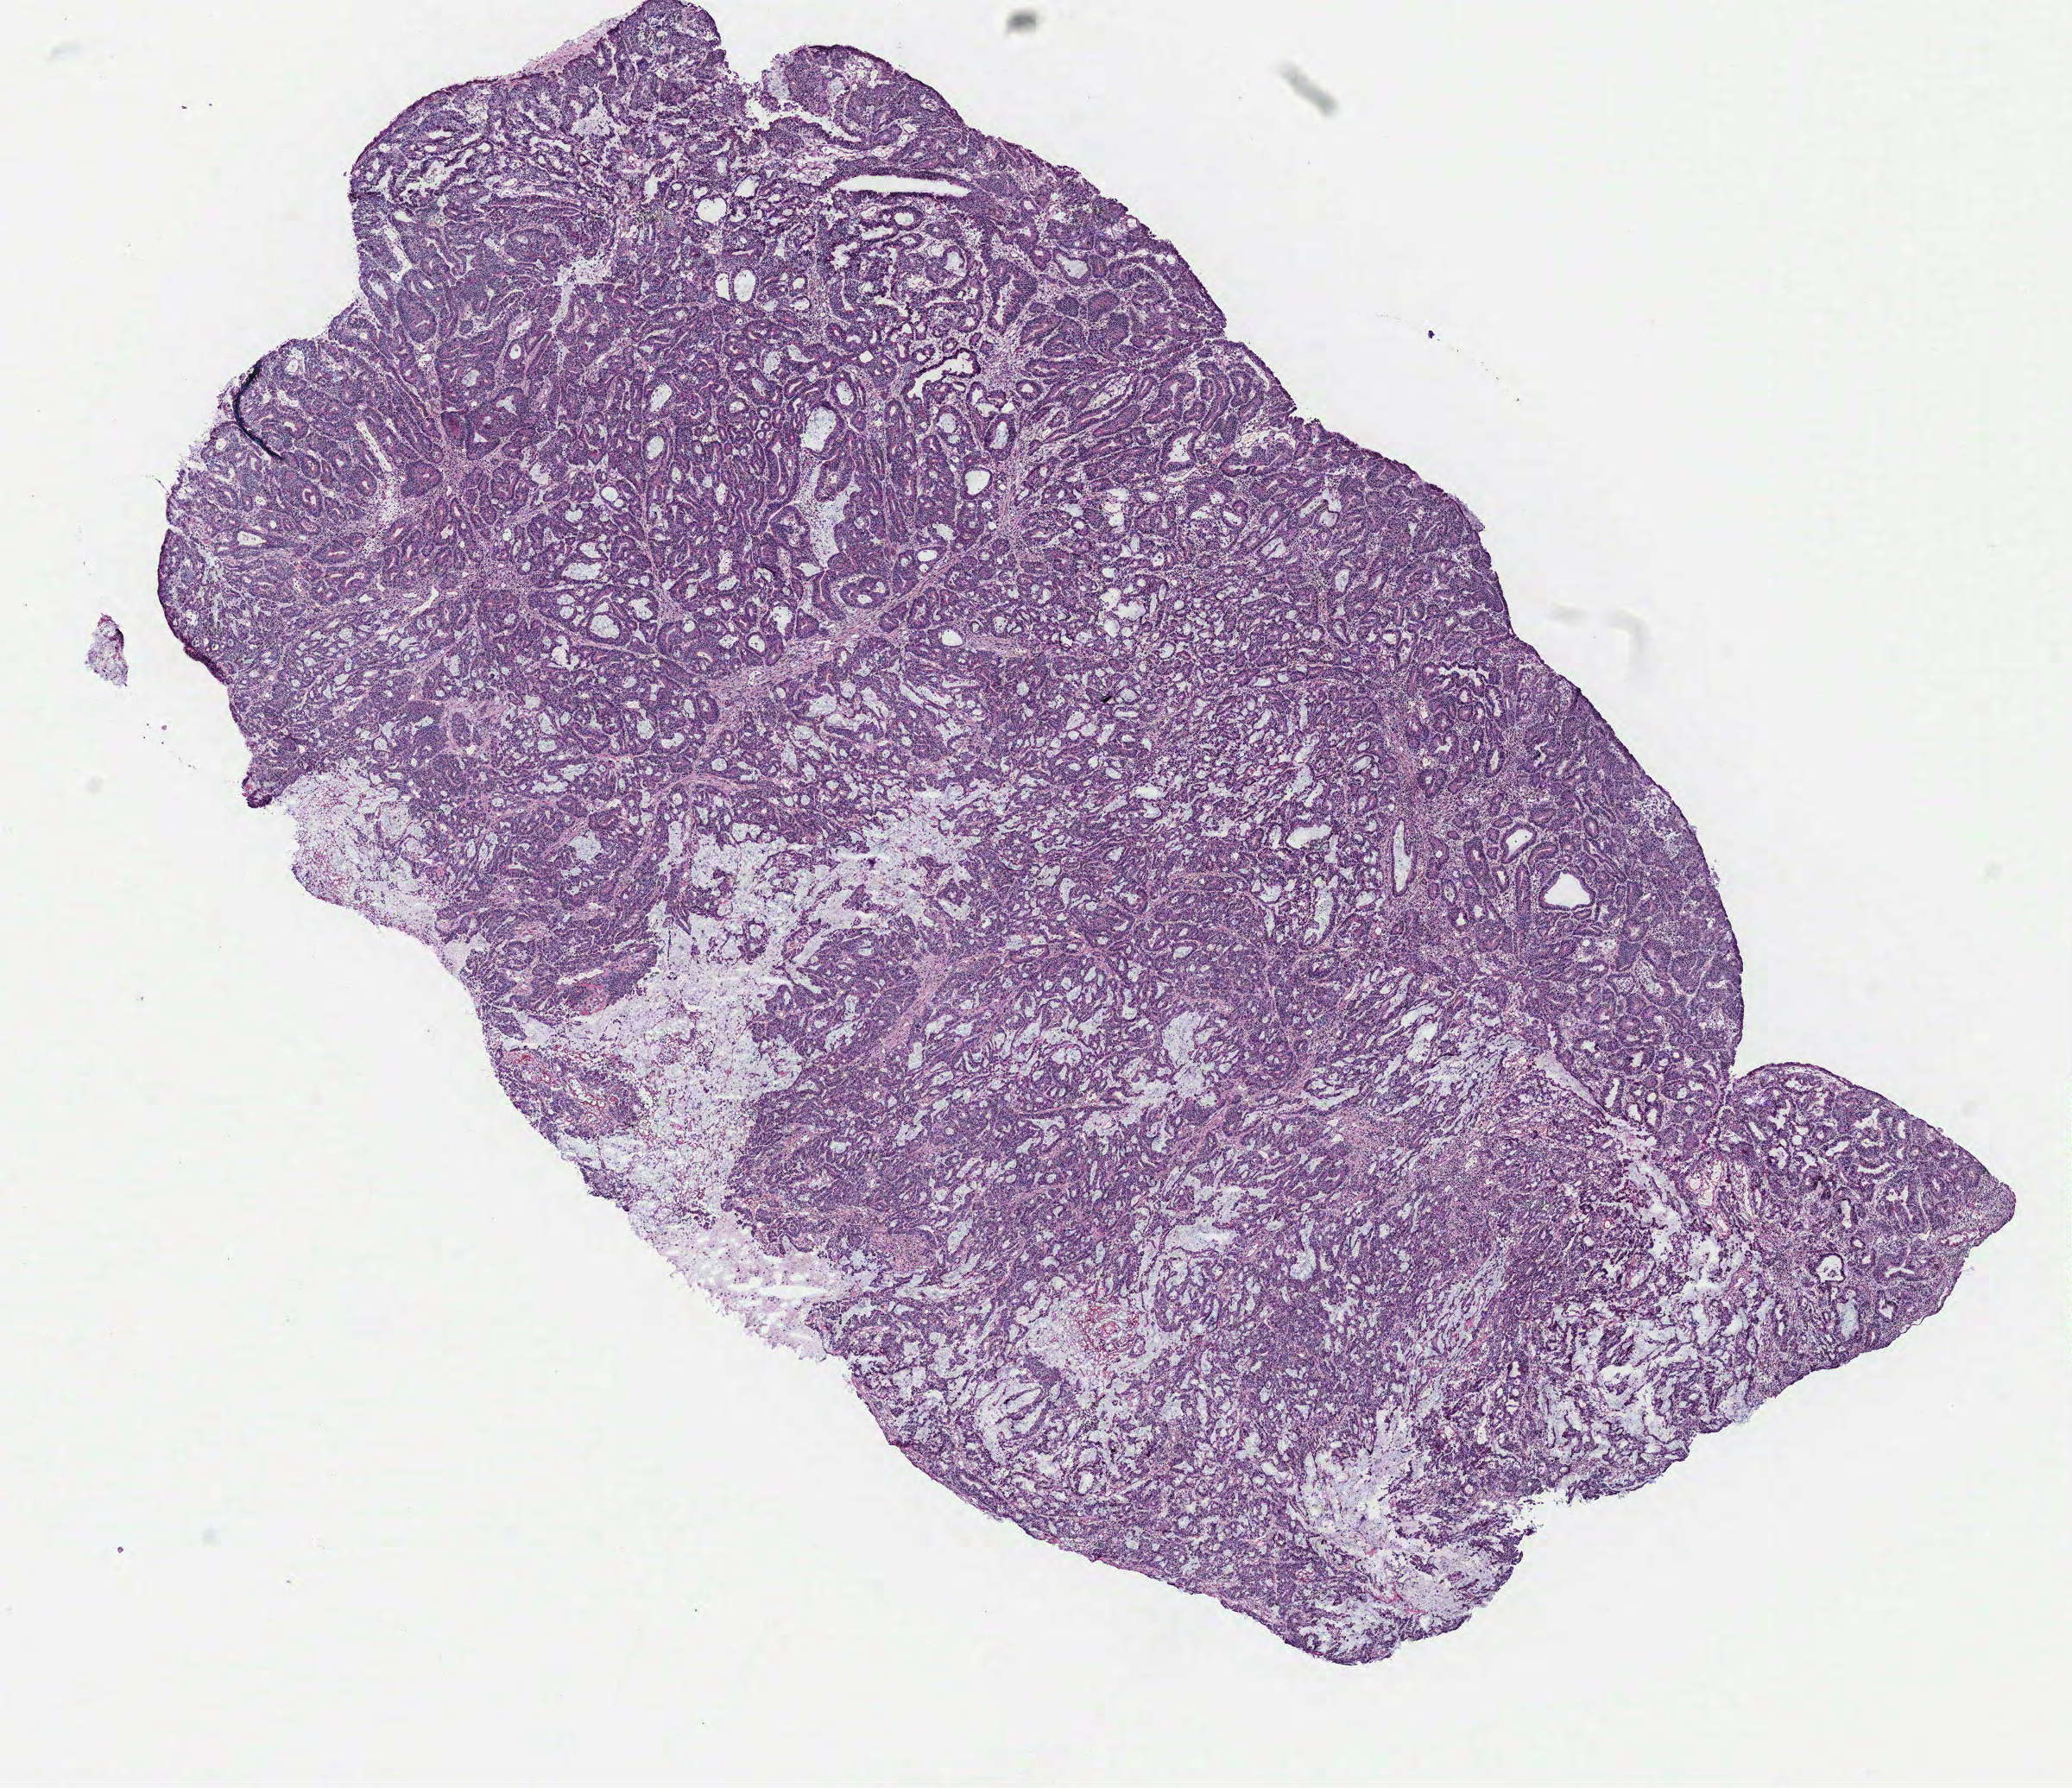
Whole-slide histology image, H&E — low-resolution overview of the scanned area, about 9.6 x 8.3 mm (acquisition: 40x scan); colon, tumour tissue. 74-year-old female patient.
* primary tumour site (as recorded): colon
* histologic diagnosis: Adenocarcinoma, NOS
* AJCC pathologic stage: IIIB